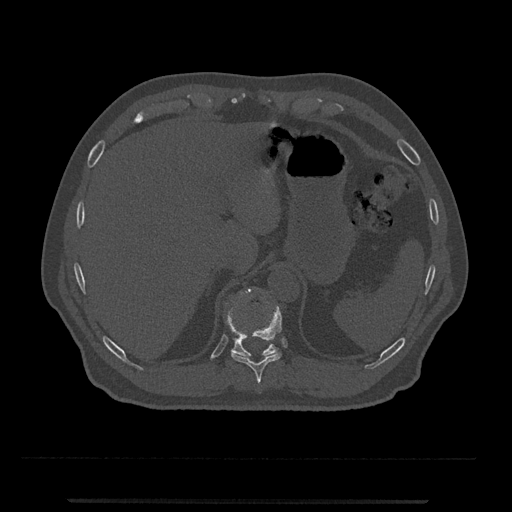
CT including the spine, one axial slice. Slice 496 of 797 in the series (ordered by position). 120 kVp. Bone window (W 1800 / L 400 HU). 0.5 mm slice thickness. 512 × 512 image matrix, field of view 419 × 419 mm. Male patient, age 63 years. From the clinical record (not read from this slice): primary cancer: prostate.
Outlined on this slice (semi-automatically segmented with operator editing):
- T10 vertebra: bounding box <231,306,282,384> (left, top, right, bottom; pixels)
- T11 vertebra: <225,288,279,356>